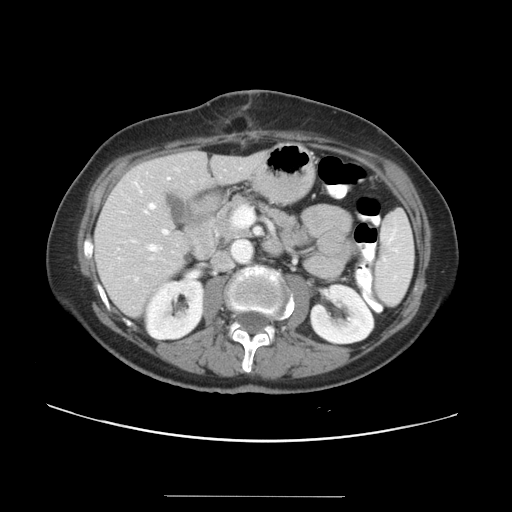
Contrast-enhanced abdominal CT, one axial slice. Slice 14 of 34 in the series (ordered by position). Reconstruction kernel STANDARD. 120 kVp. Intravenous contrast given. Soft-tissue window (W 400 / L 40 HU). 512 × 512 image matrix. Female patient, age 69 years. From the clinical record (not read from this slice): diagnosis: colorectal cancer liver metastases, imaged before liver resection; multiple liver metastases: yes; largest metastasis: 1.4 cm.
Annotated regions visible in this slice (manually delineated by an expert):
- hepatic veins: bounding box [x1, y1, x2, y2] px = [132, 177, 170, 251]
- liver: [95, 152, 263, 315]
- planned liver remnant (the part of the liver to remain after resection): [96, 152, 263, 315]
- portal vein (with intrahepatic branches): [162, 207, 254, 234]